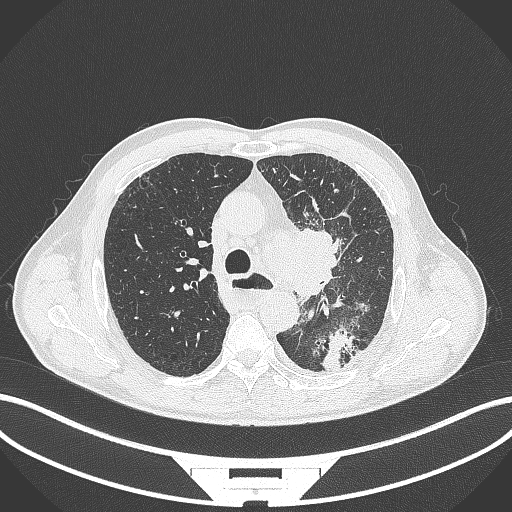
Chest CT, one axial slice. Position 266 of 411 along the scan axis. Reconstruction kernel B70f. 120 kVp. Lung window (W 1500 / L -600 HU). 1 mm slice thickness. 512 × 512 image matrix, field of view 400 × 400 mm. Male patient, age 57 years. From the clinical record (not read from this slice): clinical TNM (as recorded): T2a N1 M0.
Structures marked on this image (bounding box drawn by a radiologist):
- lung tumour (recorded histology: squamous cell carcinoma): bounding box (x1, y1, x2, y2) in pixels: (293, 225, 358, 305)